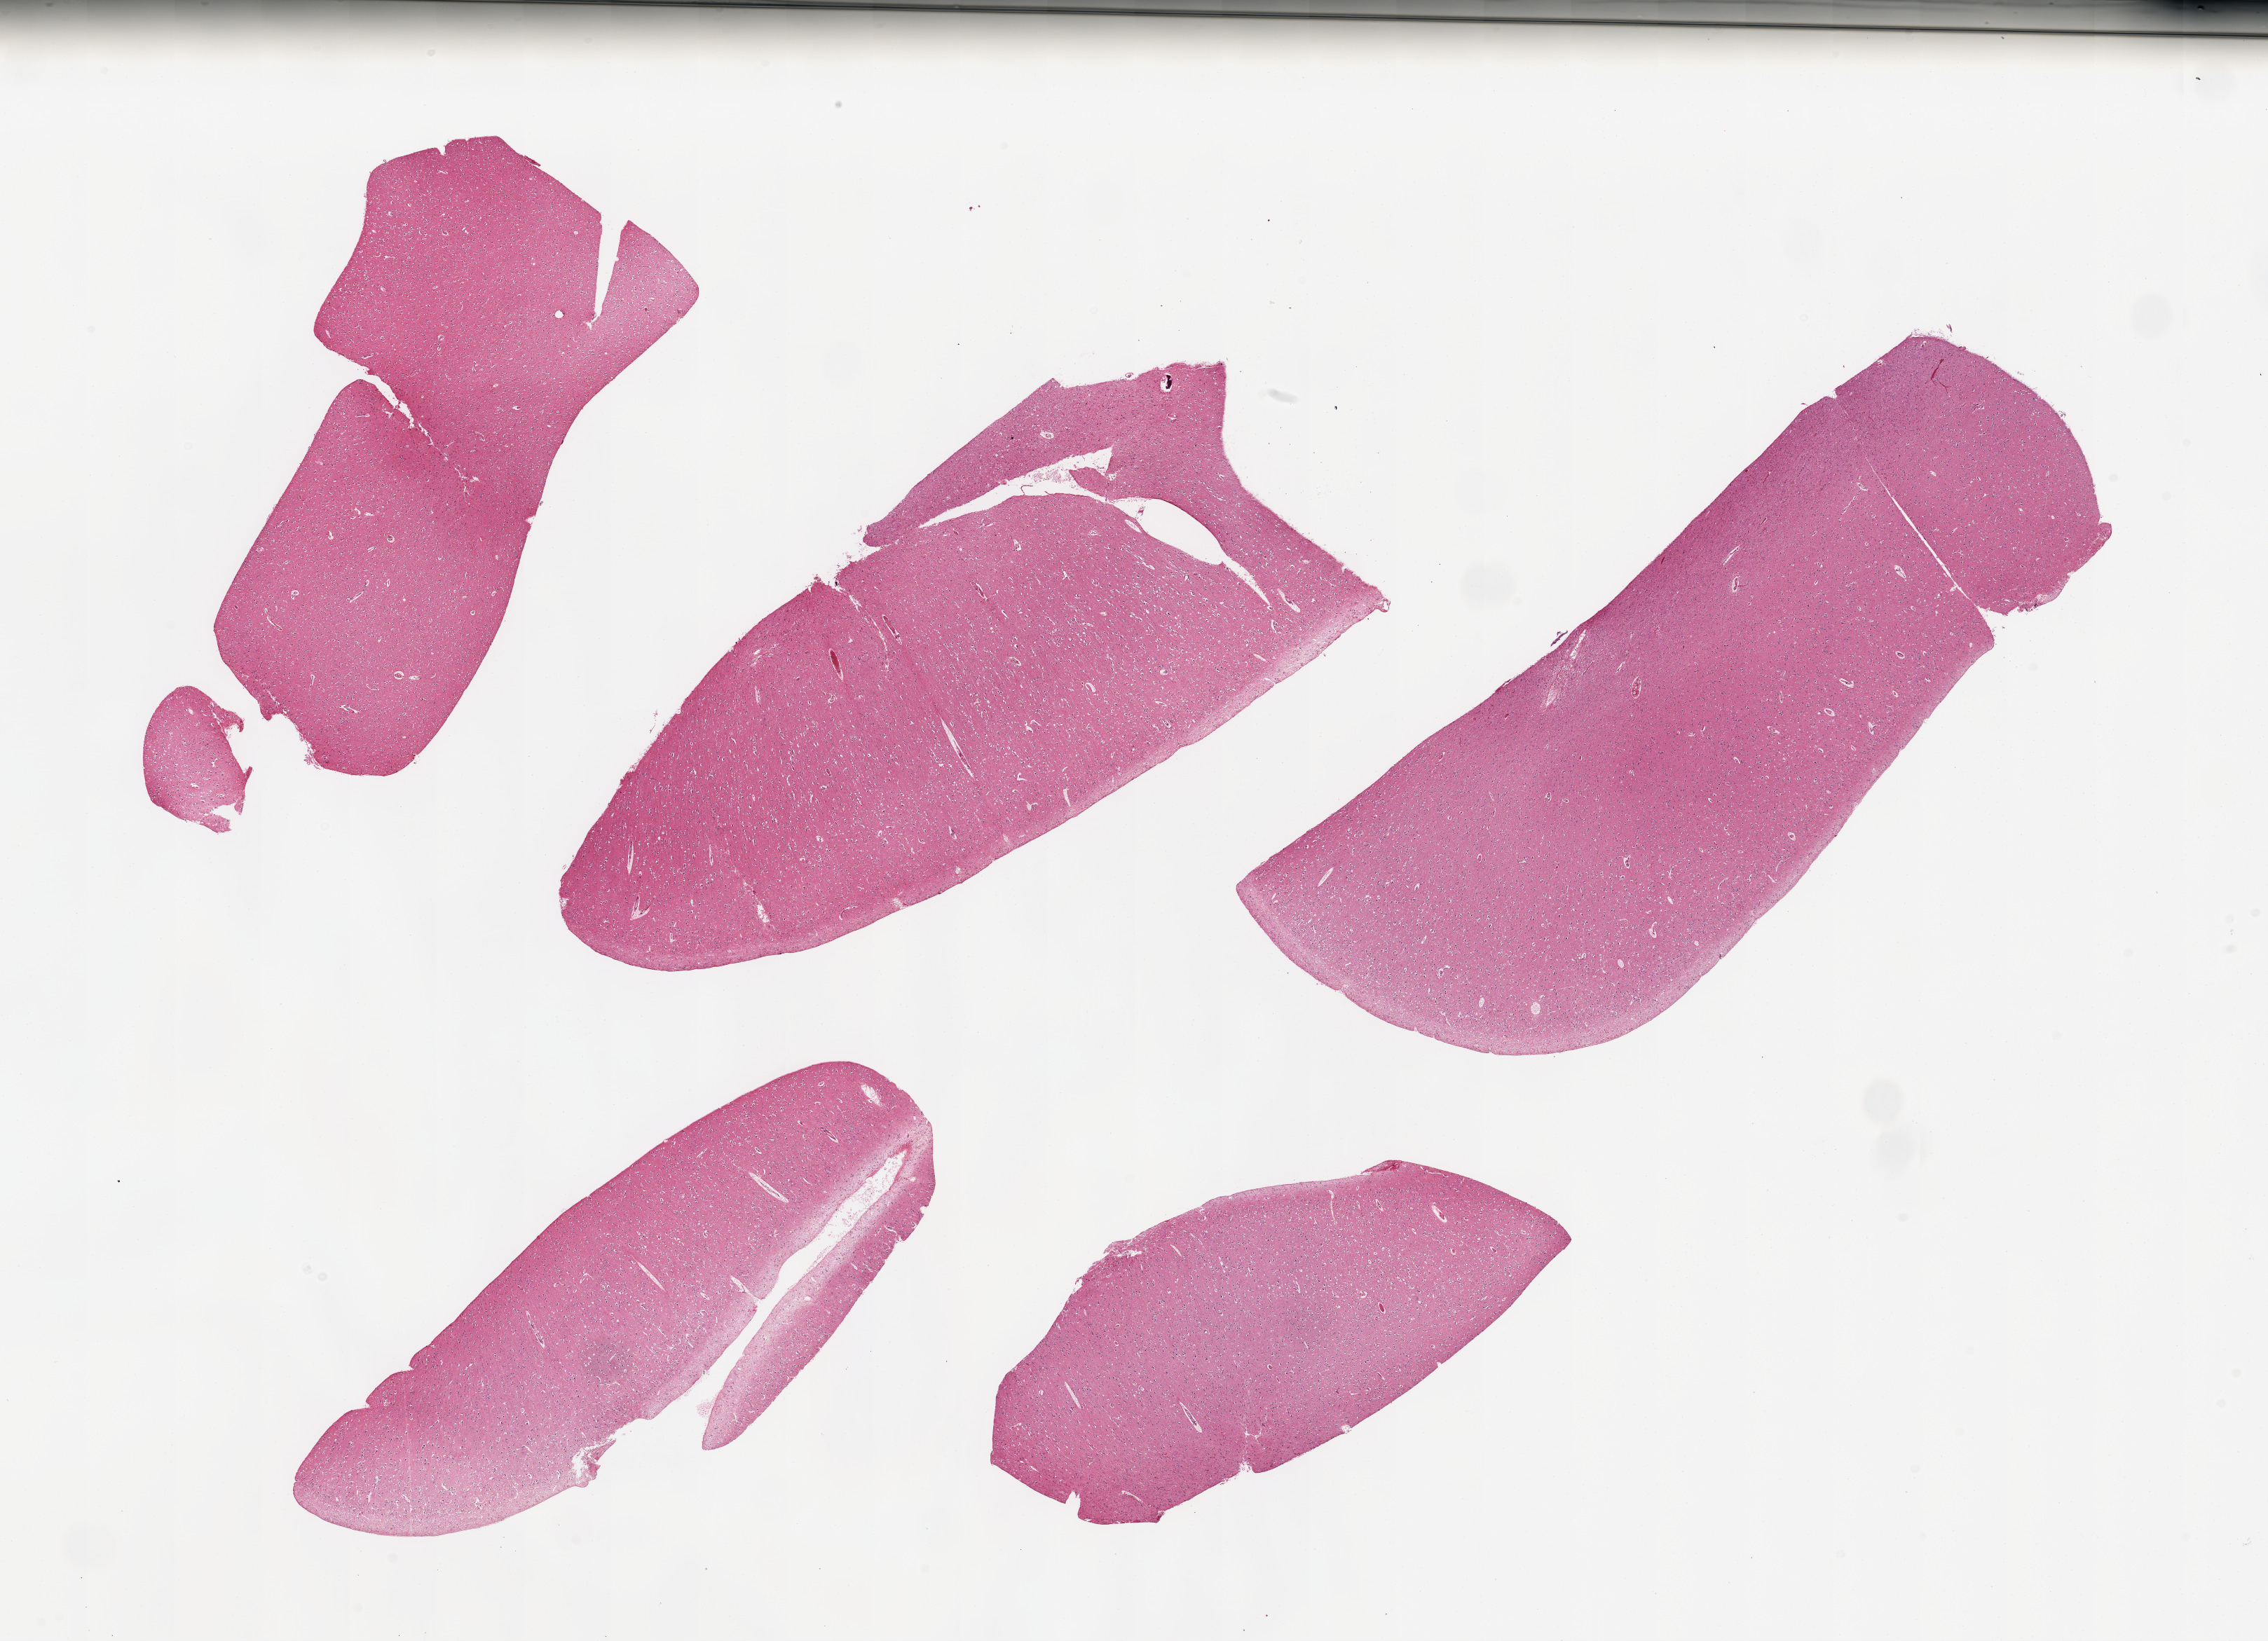
Whole-slide image, hematoxylin and eosin (H&E) stain — low-resolution overview of the scanned area, about 25.6 x 18.5 mm. PAXgene-fixed, paraffin-embedded tissue. Section of cerebral cortex (target tissue). Donor tissue sample. Donor sex: female.
- review note (as recorded): 5 pieces, no abnormalities